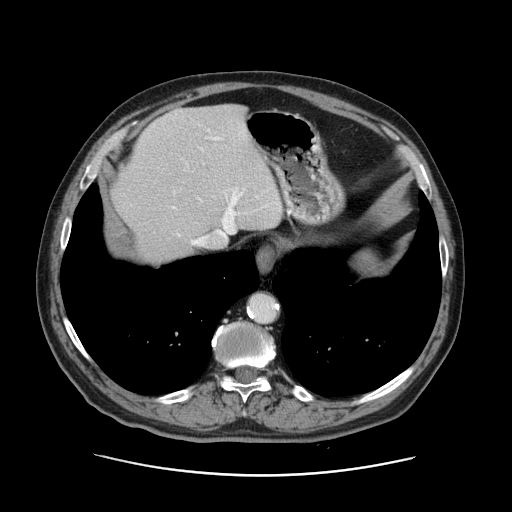
Contrast-enhanced abdominal CT, one axial slice; 120 kVp; intravenous contrast given; soft-tissue window (W 400 / L 40 HU); 512 × 512 image matrix, field of view 395 × 395 mm. Male patient, age 72 years. Case-level facts recorded for this patient, not image findings: diagnosis: colorectal cancer liver metastases, imaged before liver resection; multiple liver metastases: yes; largest metastasis: 5.4 cm; disease in both lobes: yes.
Outlined on this slice (manually delineated by an expert):
- hepatic veins: bounding box [x1, y1, x2, y2] px = [172, 130, 275, 246]
- liver: [113, 104, 283, 263]
- planned liver remnant (the part of the liver to remain after resection): [147, 104, 283, 263]
- portal vein (with intrahepatic branches): [225, 189, 245, 219]